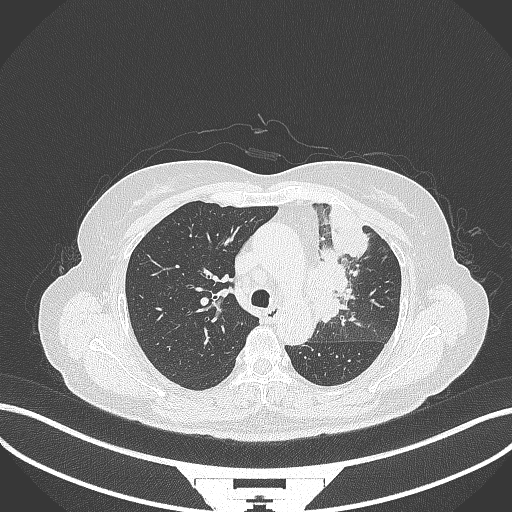
Chest CT, one axial slice; reconstruction kernel B70f; lung window (W 1500 / L -600 HU); 1 mm slice thickness; 512 × 512 image matrix, field of view 400 × 400 mm. Patient: female, 64 years. From the clinical record (not read from this slice): clinical TNM (as recorded): T2a N2 M0.
Annotated regions visible in this slice (rectangle marked by the reading radiologist):
- lung tumour (recorded histology: adenocarcinoma): bounding box [x1, y1, x2, y2] px = [306, 219, 369, 324]